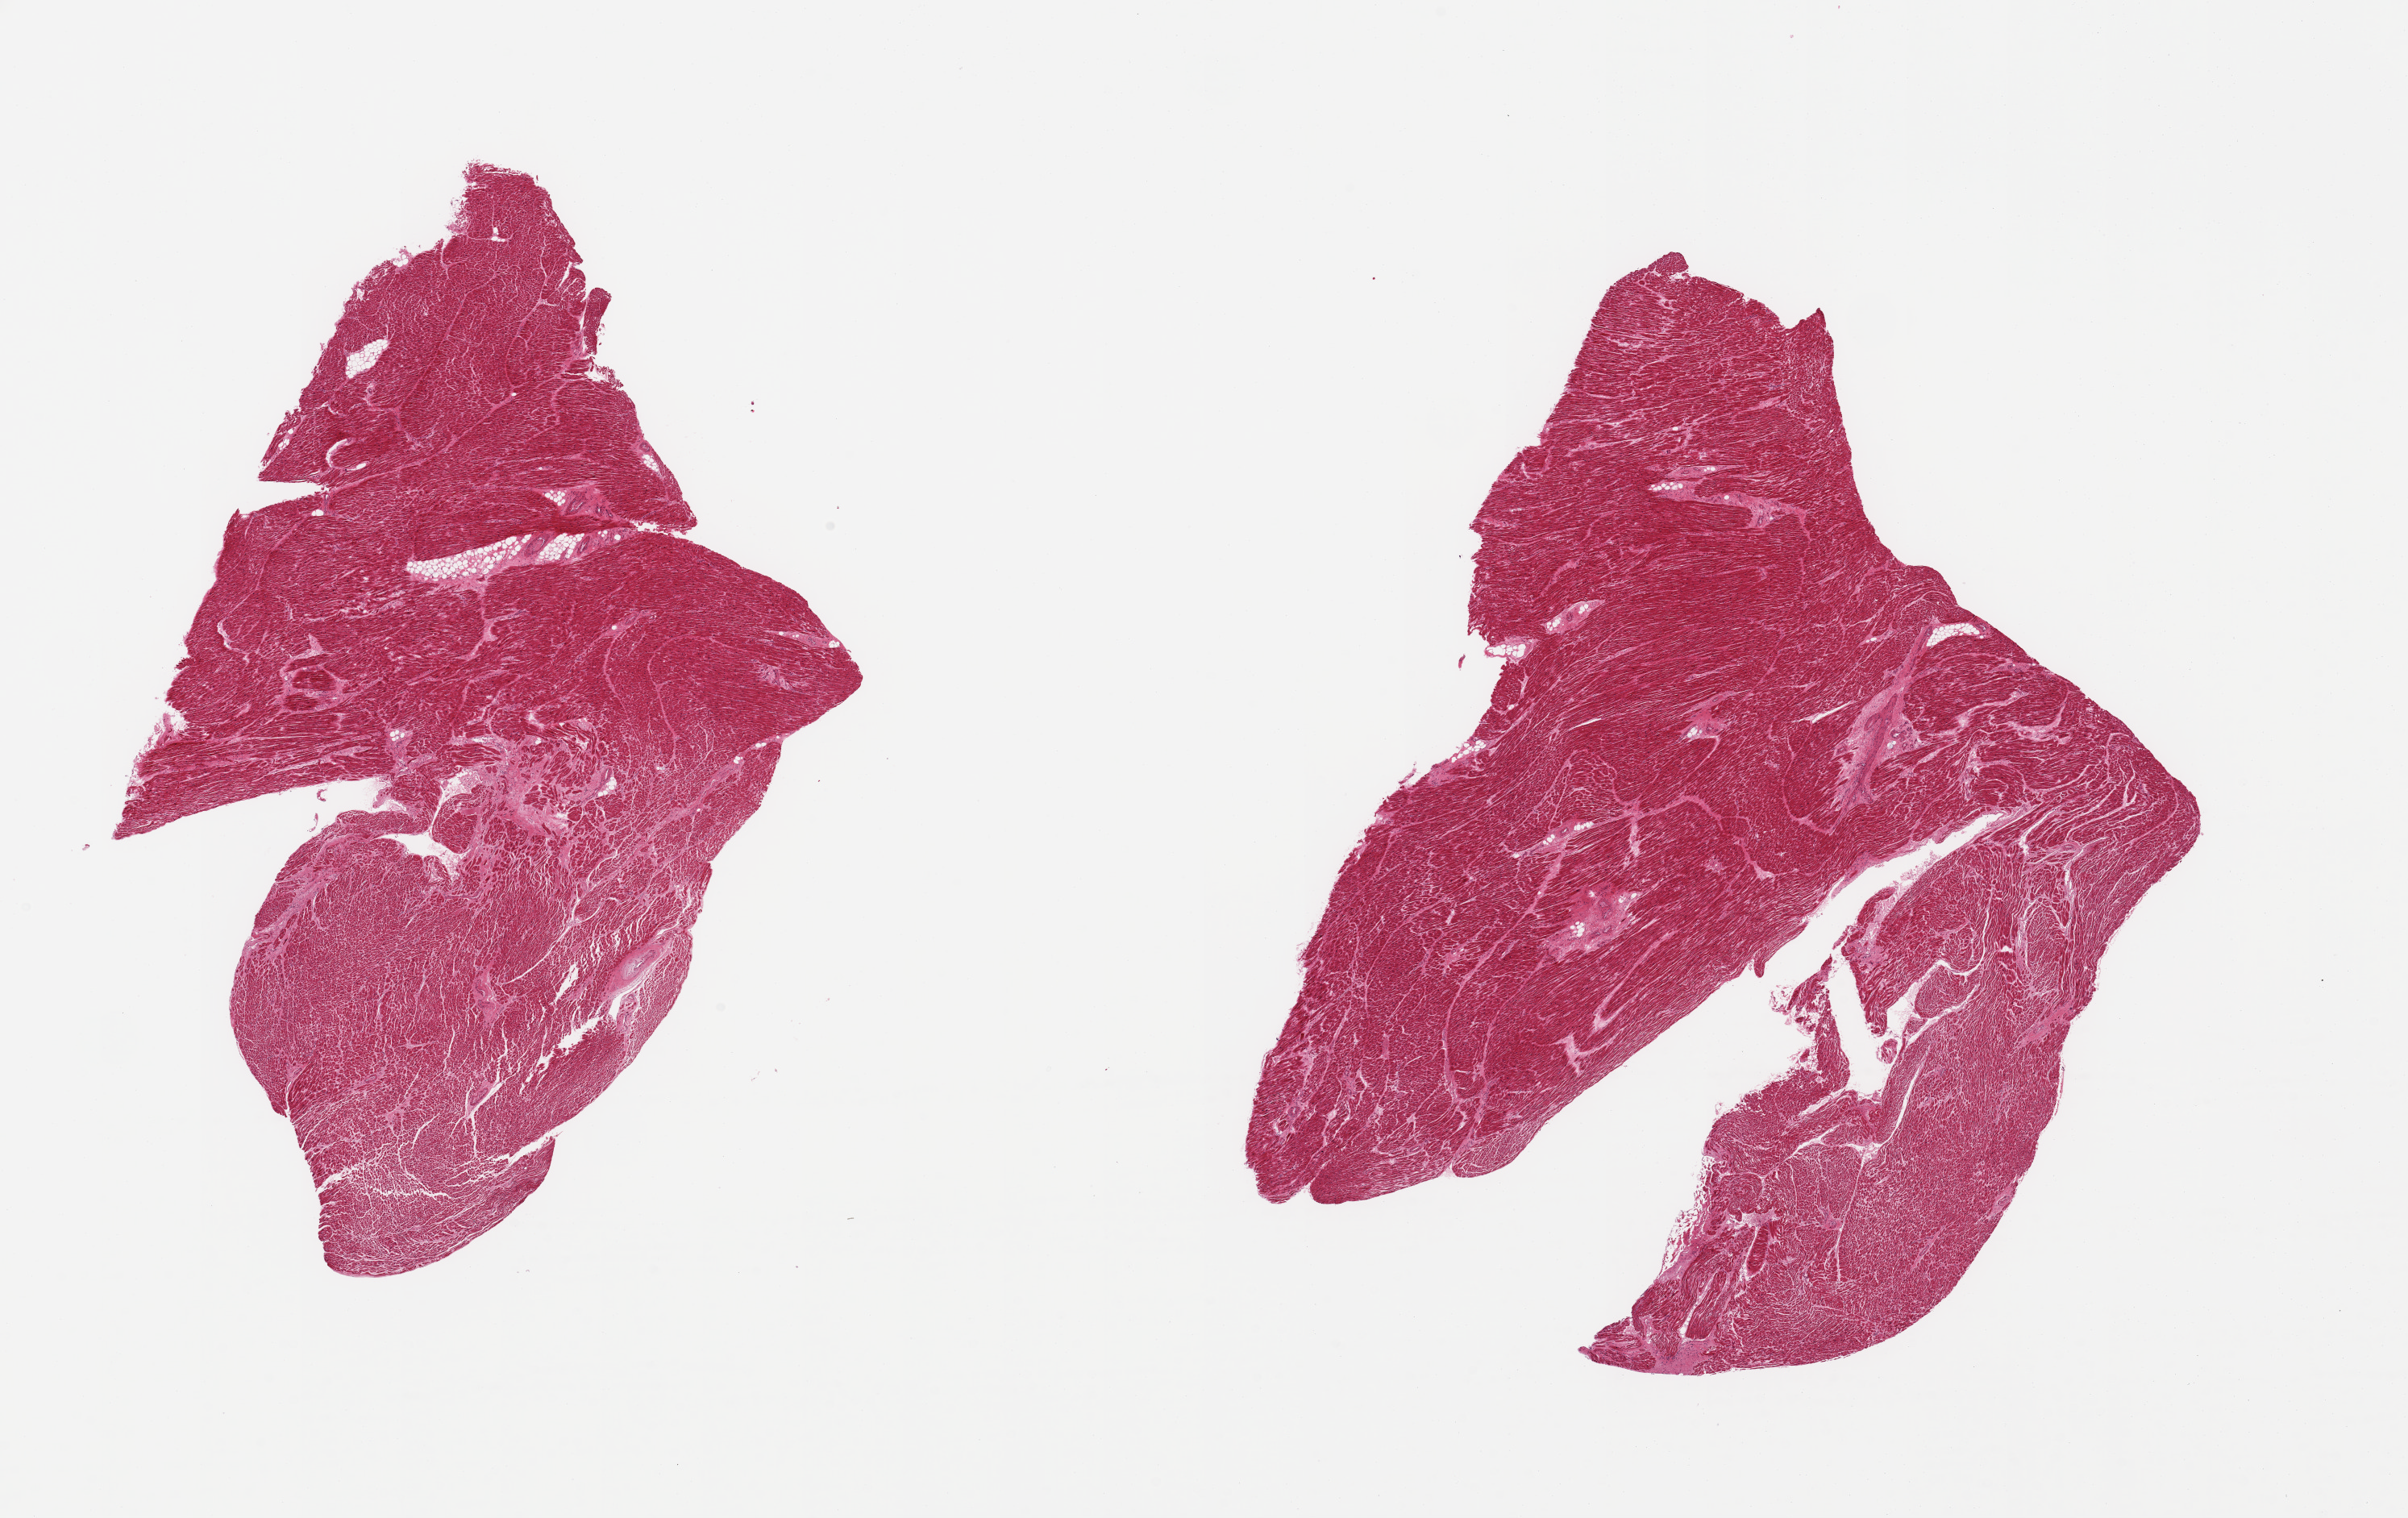
Whole-slide image, hematoxylin and eosin (H&E) stain, brightfield — low-resolution overview of the scanned area, about 23.6 x 14.9 mm, PAXgene-fixed, paraffin-embedded tissue, section of heart (target tissue), donor tissue sample. Female donor.
* review note (as recorded): 2 pieces; several small foci of fibrosis